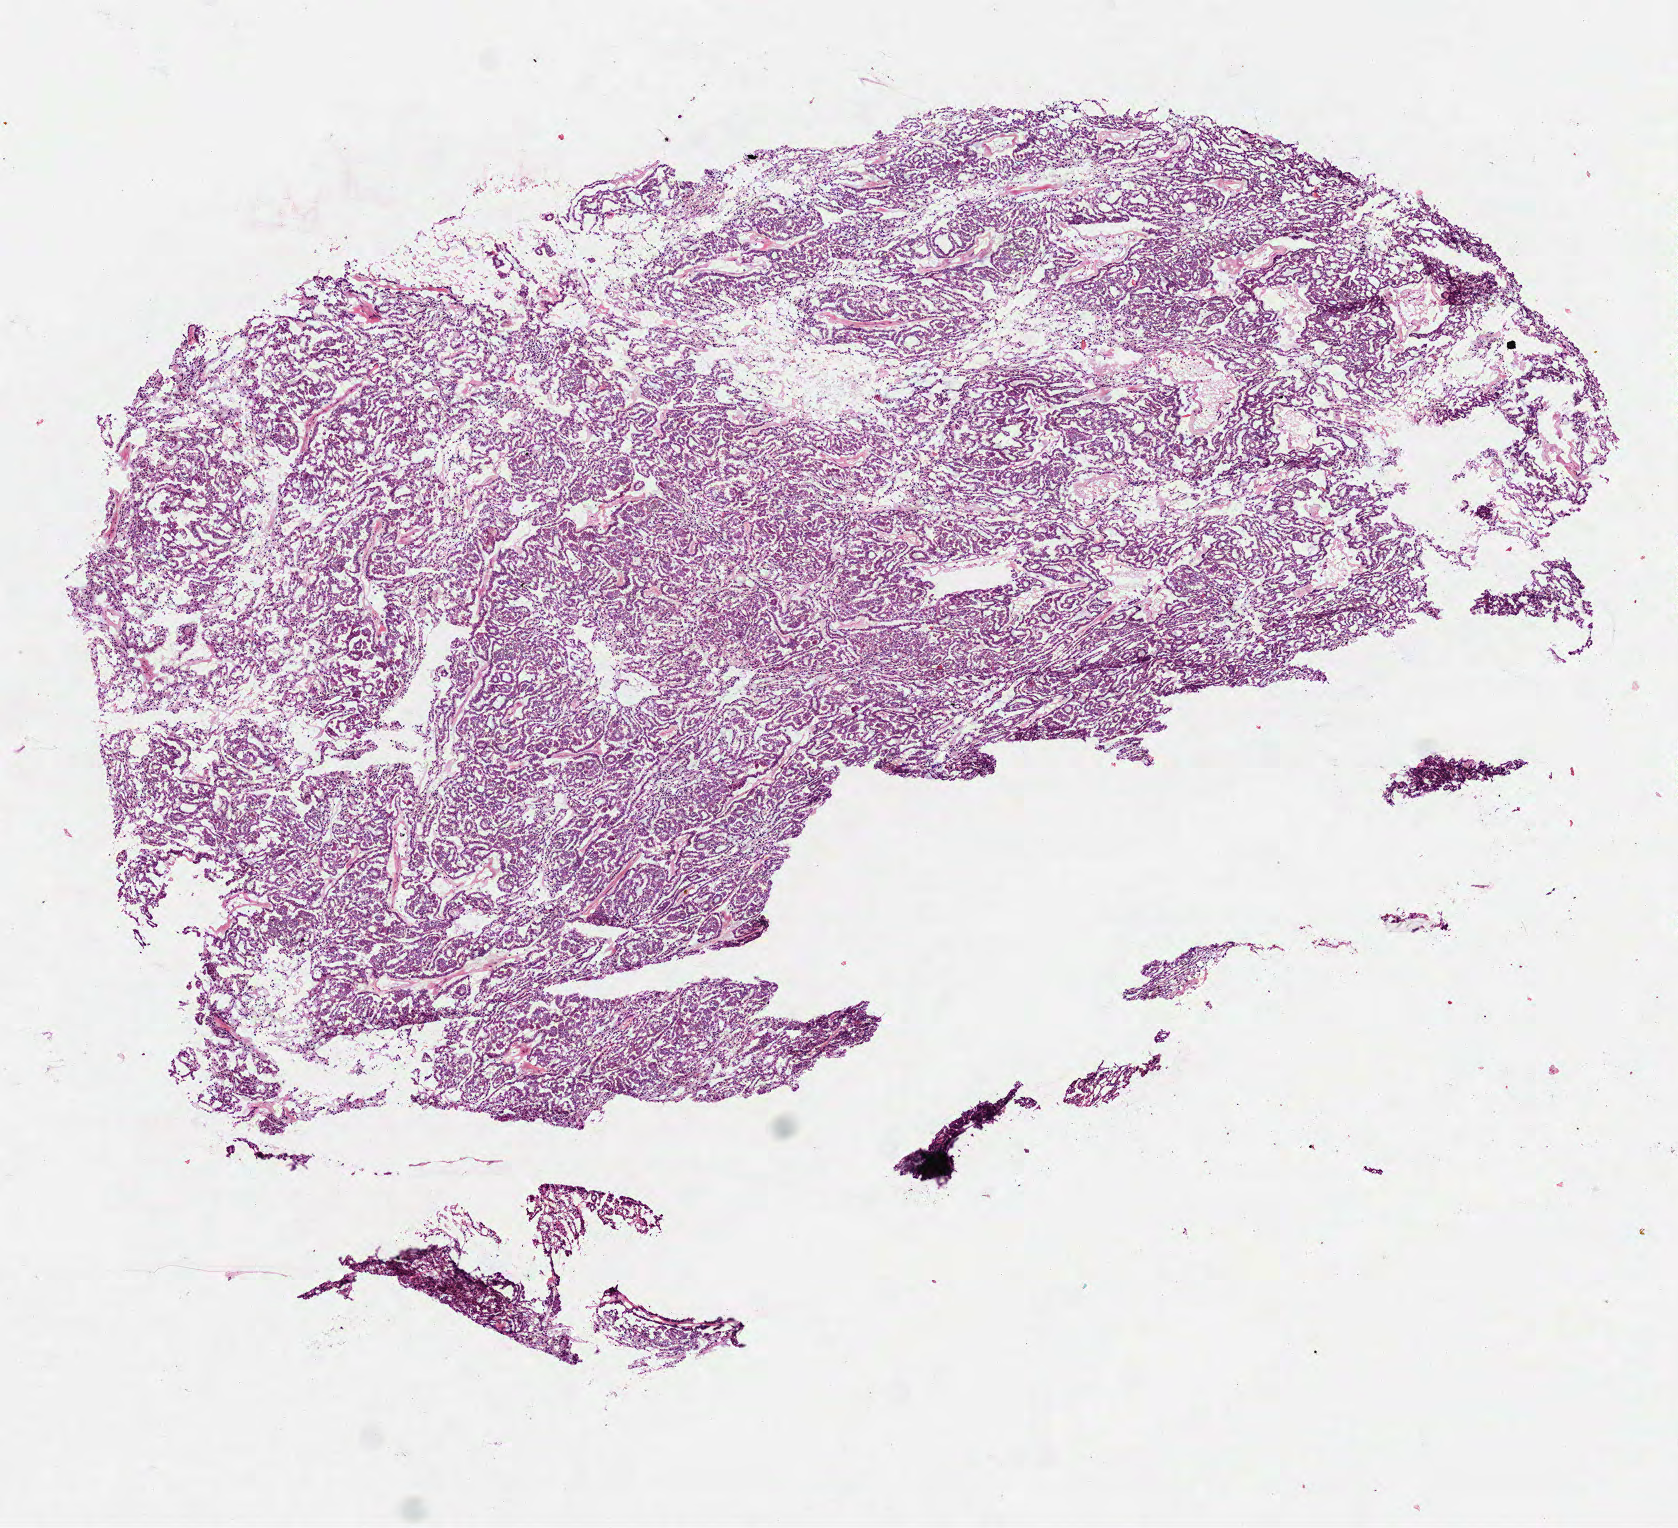
Whole-slide histology image, Hematoxylin and eosin (H&E) stained — whole scanned area (about 6.8 x 6.2 mm, from a 40x scan) shown as a low-resolution overview; frozen section; primary tumour sample from the kidney. Patient sex: male. Slide review estimates, as recorded: tumour cells 100%, tumour nuclei 90%, normal cells 0%, stromal cells 0%, necrosis 0%. Infiltration values recorded for this section: lymphocyte infiltration 2%, monocyte infiltration 5%, neutrophil infiltration 0%.
Pathologic diagnosis: Papillary adenocarcinoma, NOS. TNM: T2 NX M0. AJCC pathologic stage: II (6th edition). Laterality: right.